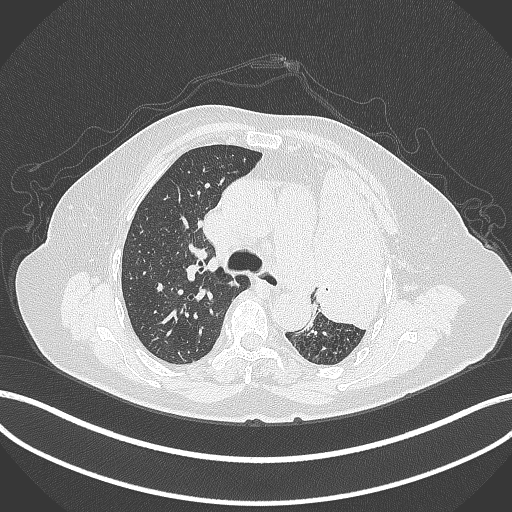
Chest CT, one axial slice. Slice 260 of 399 in the series (ordered by position). Reconstruction kernel B70f. 120 kVp. Lung window (W 1500 / L -600 HU). 1 mm slice thickness. 512 × 512 image matrix, field of view 400 × 400 mm. Patient: female, 75 years. Case-level facts recorded for this patient, not image findings: clinical TNM (as recorded): T3 N3 M1.
Annotated regions visible in this slice (rectangle marked by the reading radiologist):
- lung tumour (recorded histology: adenocarcinoma): bounding box <308,158,400,332> (left, top, right, bottom; pixels)